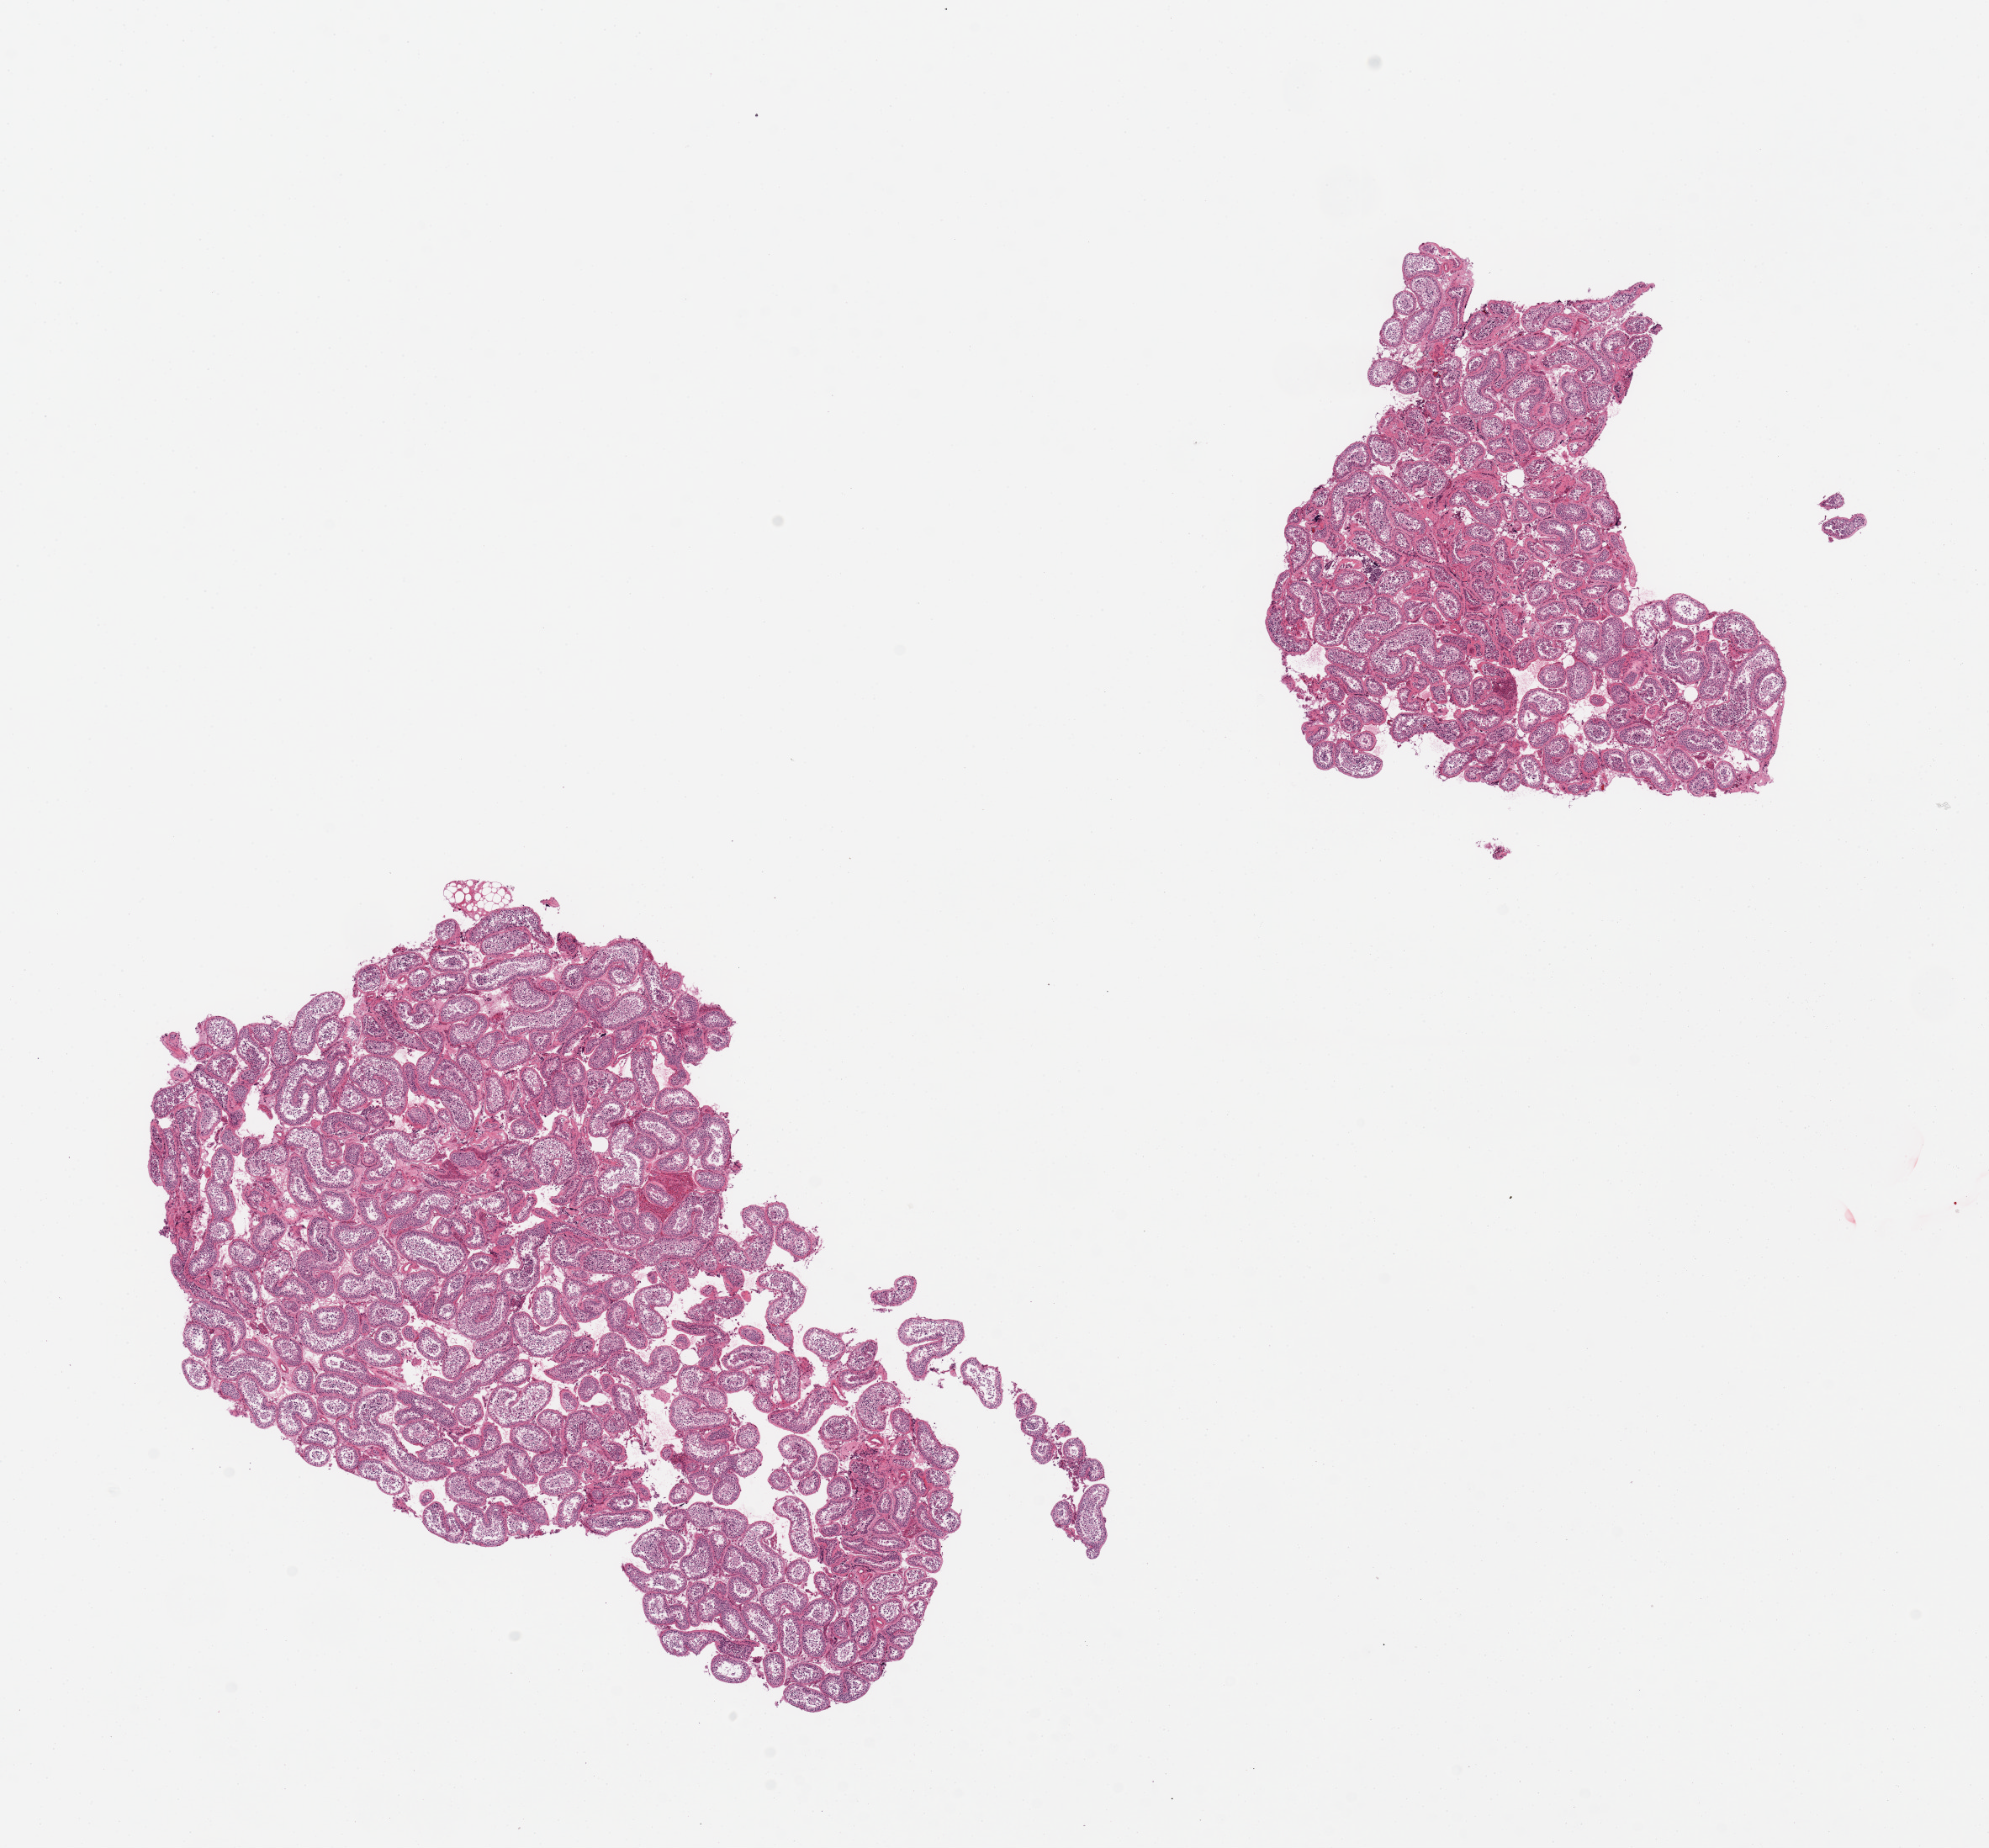
Haematoxylin and eosin whole-slide image, brightfield, low-resolution overview of the scanned area, about 18.7 x 17.4 mm (acquisition: 20x scan). PAXgene-fixed paraffin-embedded (PFPE) section. Section of testis (target tissue). Donor tissue sample. Donor: male.
• pathologist's review note for this sample: 2 pieces; spermatogenesis